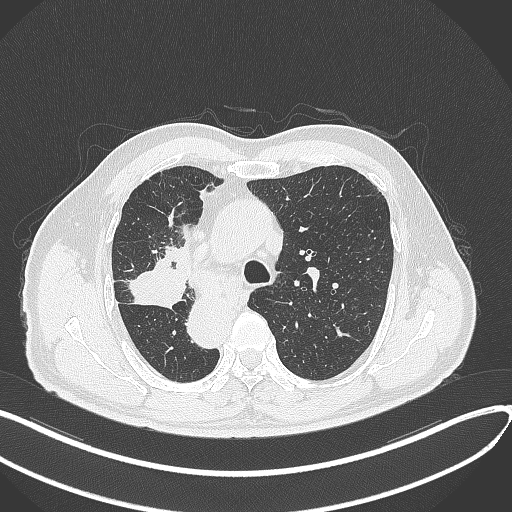
Chest CT, one axial slice. Slice 217 of 300 in the series (ordered by position). 120 kVp. Lung window (W 1500 / L -600 HU). 1 mm slice thickness. 512 × 512 image matrix. Male patient, age 67 years. Case-level facts recorded for this patient, not image findings: clinical TNM (as recorded): T2a N0 M0.
Annotated regions visible in this slice (bounding box drawn by a radiologist):
- lung tumour (recorded histology: squamous cell carcinoma): bounding box (x1, y1, x2, y2) in pixels: (127, 264, 190, 311)